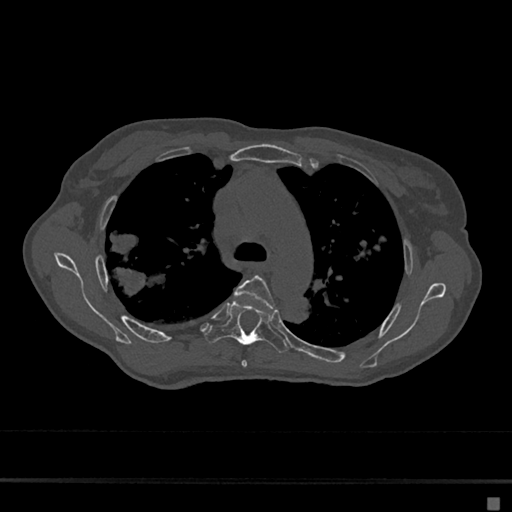
CT including the spine, one axial slice. Slice 475 of 797 in the series (ordered by position). Bone window (W 1800 / L 400 HU). 0.5 mm slice thickness. 512 × 512 image matrix, field of view 360 × 360 mm. Patient: female, 68 years. From the clinical record (not read from this slice): primary cancer: renal.
Structures marked on this image (semi-automatic segmentation, software-assisted and operator-edited):
- T4 vertebra: bounding box [x1, y1, x2, y2] px = [235, 275, 276, 367]
- T5 vertebra: [205, 301, 289, 353]